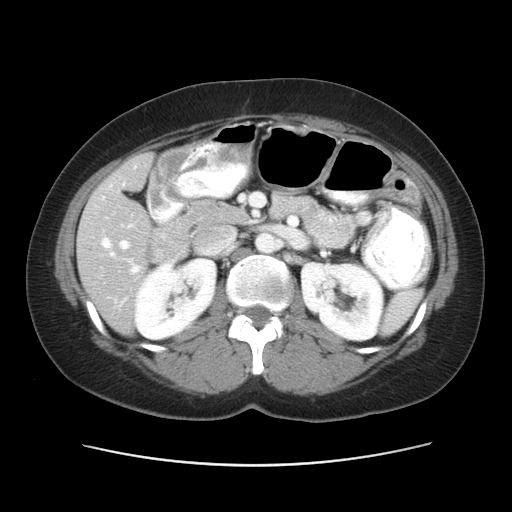
Contrast-enhanced abdominal CT, one axial slice. Slice 26 of 52 in the series (ordered by position). Reconstruction kernel STANDARD. Intravenous contrast given. Soft-tissue window (W 400 / L 40 HU). 5 mm slice thickness. 512 × 512 image matrix. Female patient, age 48 years. Case-level facts recorded for this patient, not image findings: diagnosis: colorectal cancer liver metastases, imaged before liver resection; multiple liver metastases: yes; largest metastasis: 4.5 cm; disease in both lobes: yes.
Structures marked on this image (manually delineated by an expert):
- hepatic veins: box from (x=102, y=224) to (x=140, y=273) px
- liver: (x=78, y=155)–(x=151, y=333)
- portal vein (with intrahepatic branches): (x=119, y=183)–(x=130, y=249)
- liver metastasis: (x=83, y=246)–(x=91, y=252)